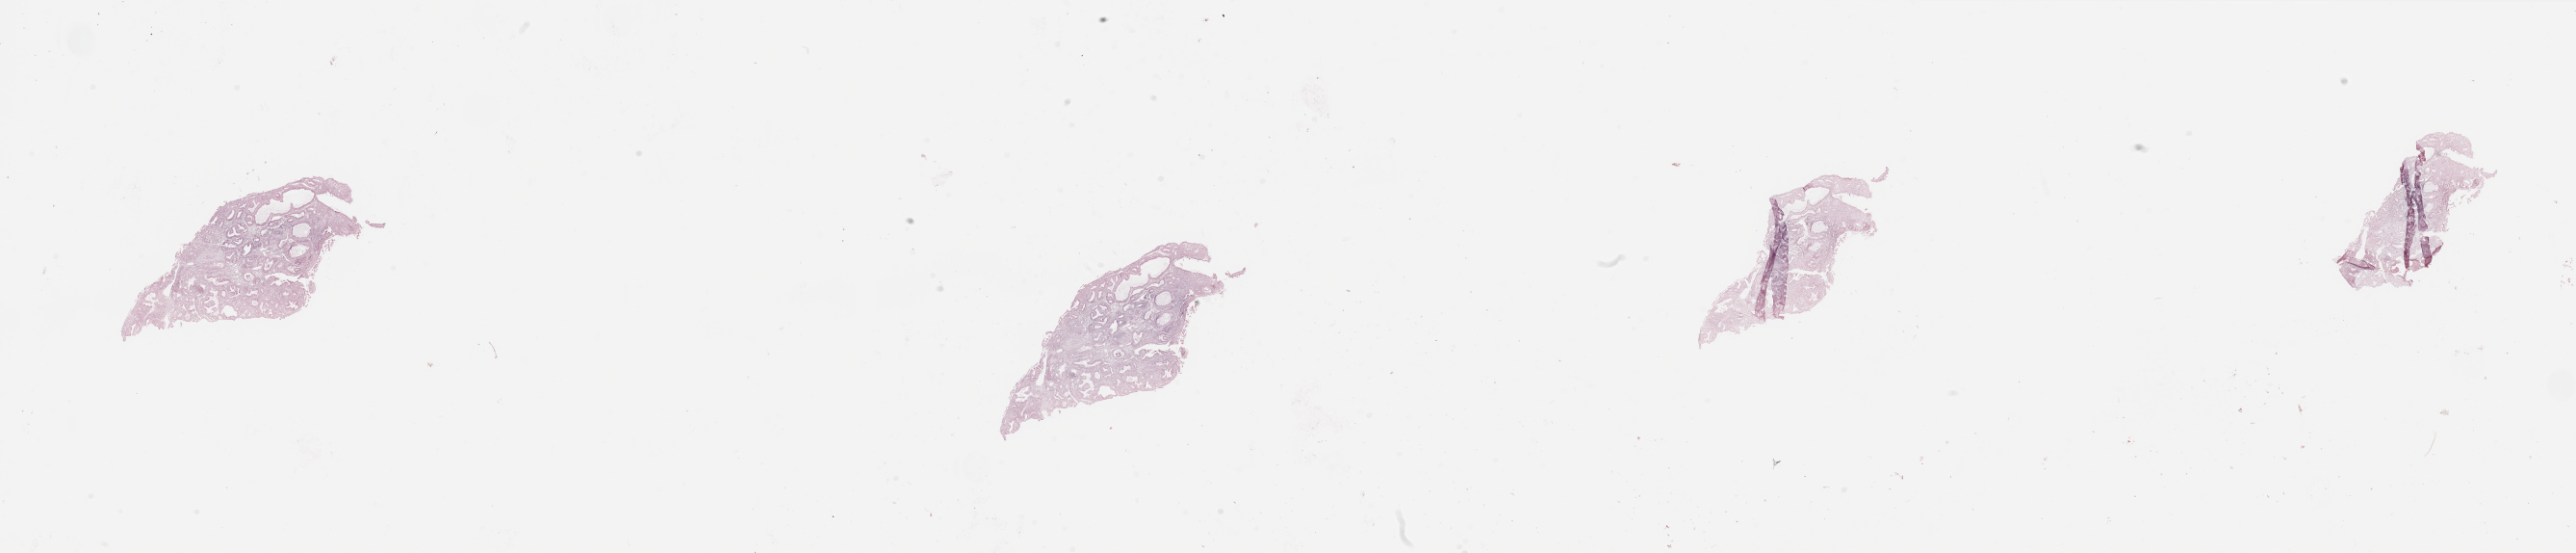
Whole-slide histology image, Hematoxylin and eosin (H&E) stained, whole scanned area (about 42.3 x 9.1 mm) shown as a low-resolution overview. Tumour tissue sample, sampled site: uterus. 67-year-old female patient.
Diagnosis: Endometrioid adenocarcinoma, NOS.